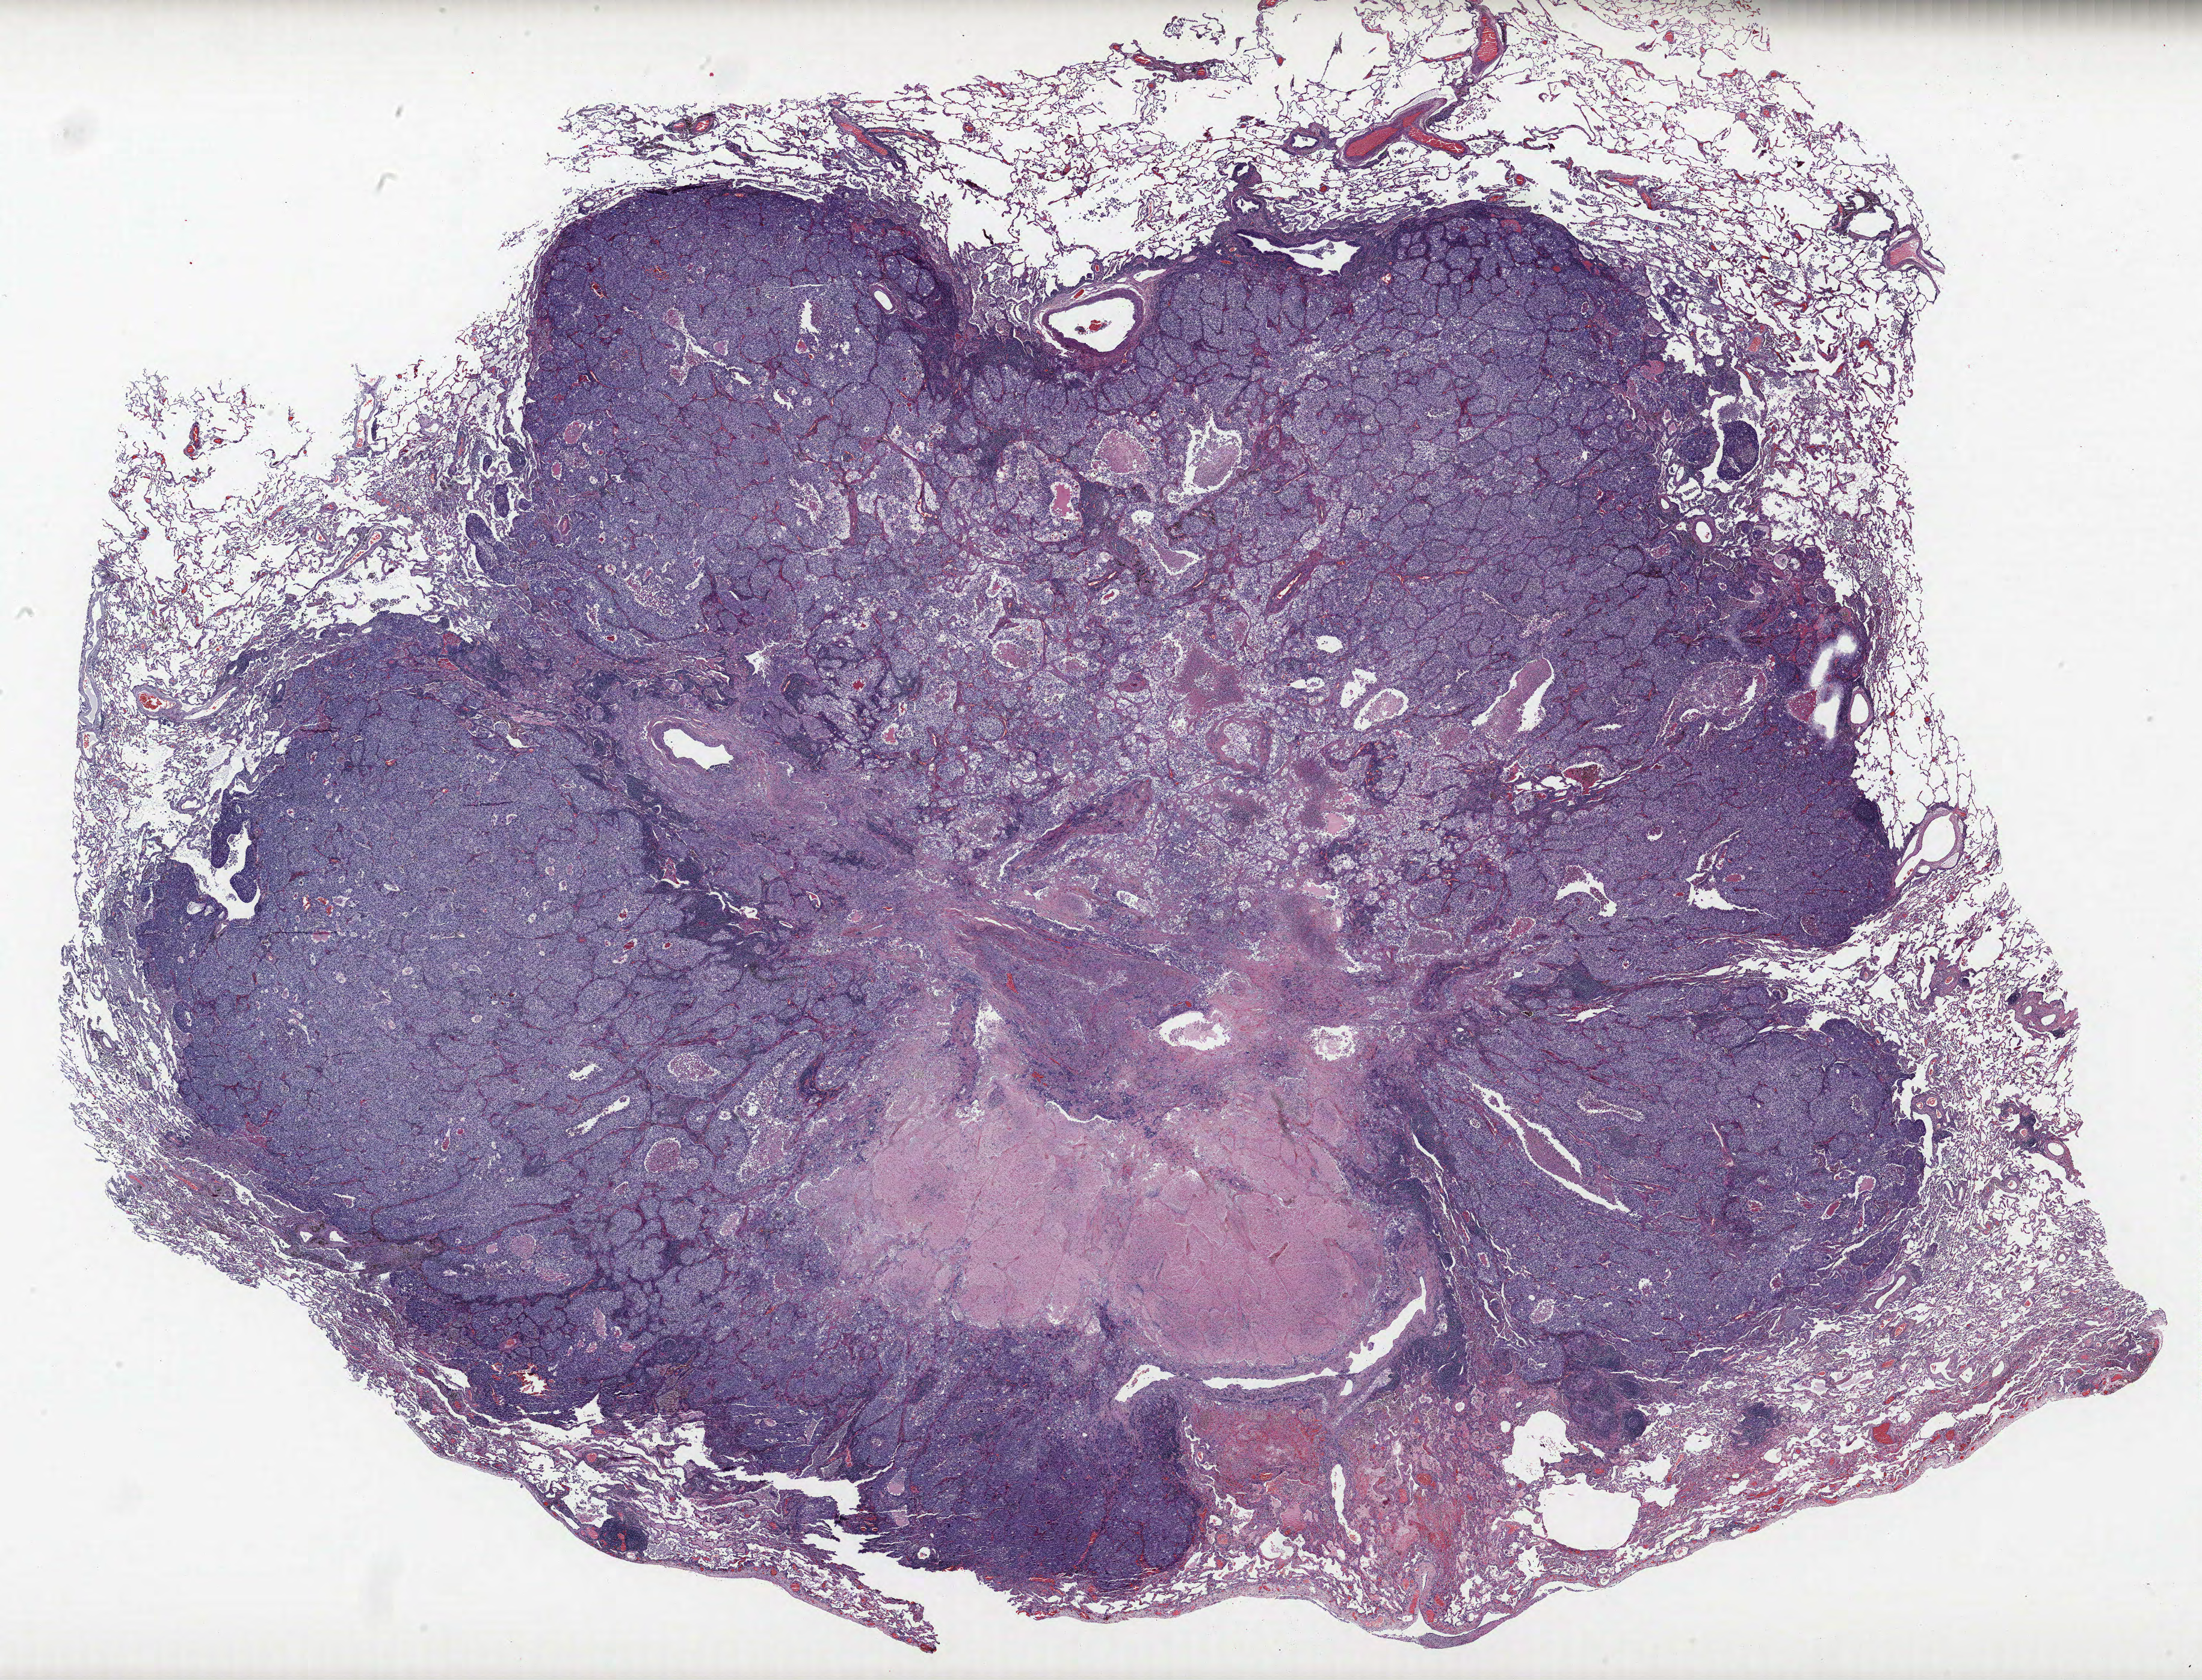
H&E whole-slide image, whole scanned area (about 29.3 x 22.3 mm) shown as a low-resolution overview. Formalin-fixed paraffin-embedded (FFPE) section. Lung tissue. Male patient, aged 62 at enrolment. Current smoker at enrolment. Grade: poorly differentiated (G3).
Stage (AJCC 6th edition): IB. Participant's lung-cancer diagnosis: Adenocarcinoma, NOS. Tumour size (pathology): 32 mm. Primary tumour location (clinical record): left upper lobe.